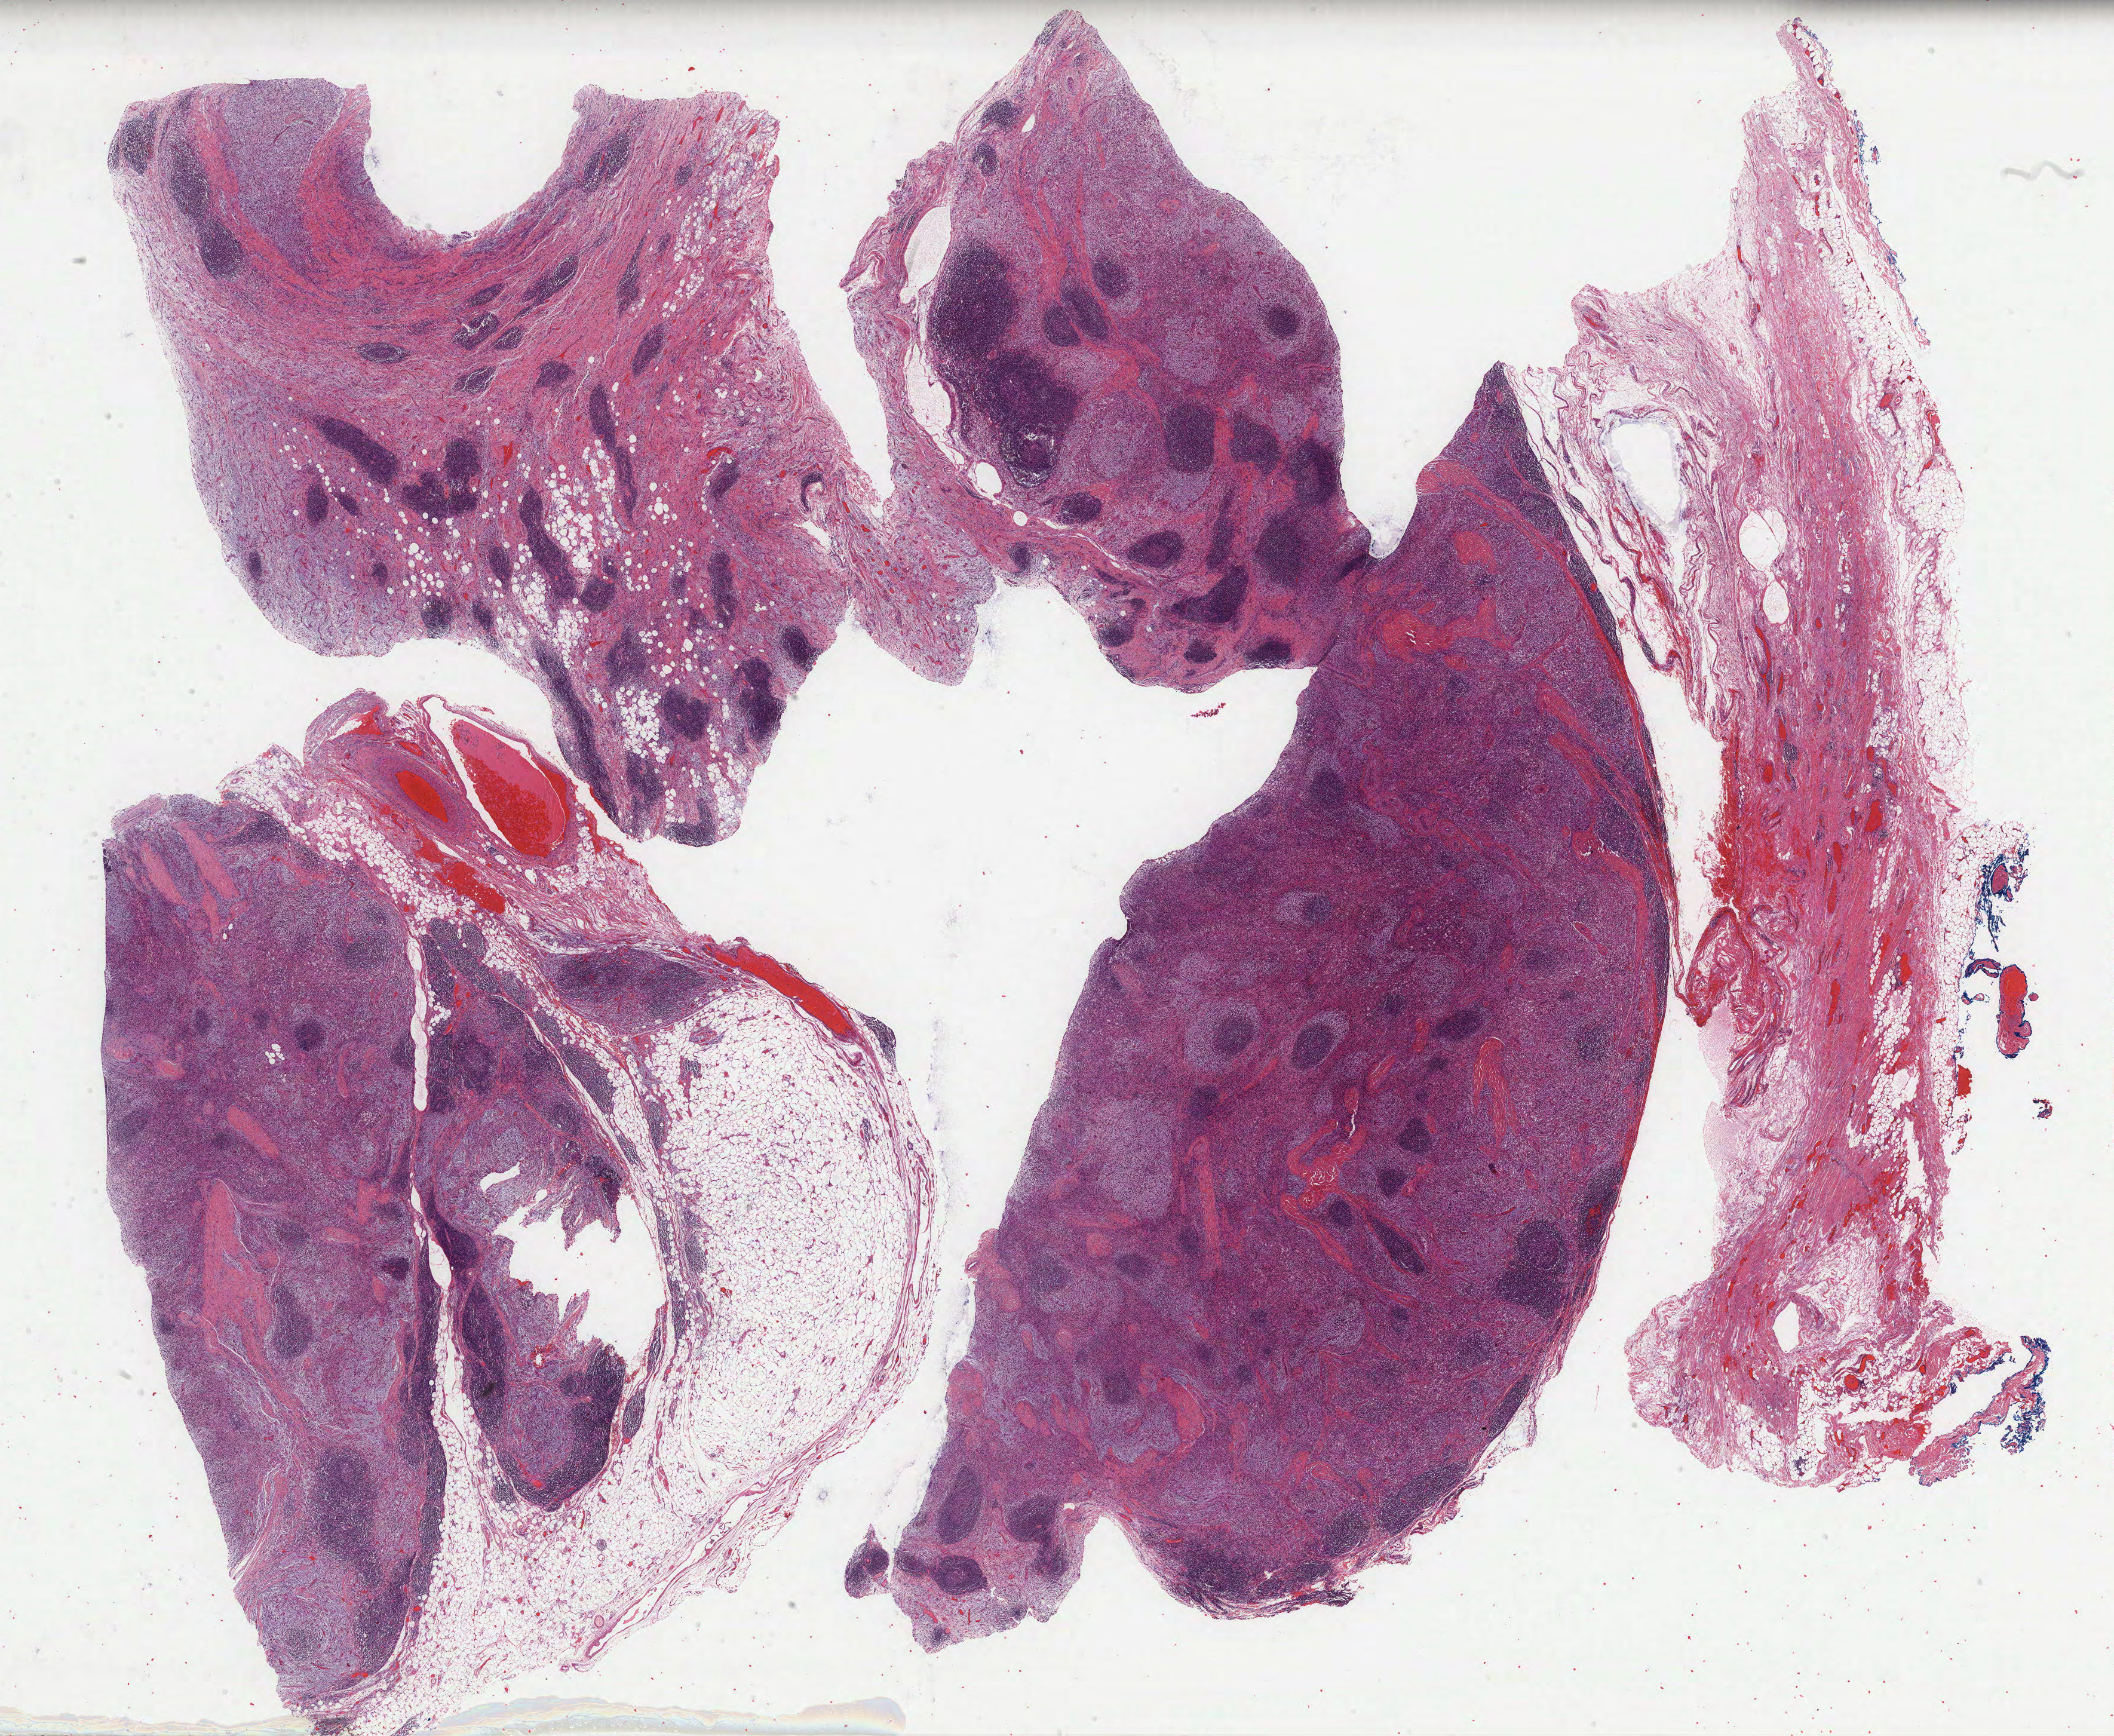
Whole-slide histology image, Hematoxylin and eosin (H&E) stained, low-resolution overview of the scanned area, about 28.6 x 23.5 mm; formalin-fixed paraffin-embedded (FFPE) diagnostic section; primary tumour sample from the connective, subcutaneous and other soft tissues. Male patient; age at initial diagnosis 68 years.
* pathologic diagnosis: Dedifferentiated liposarcoma (connective, subcutaneous and other soft tissues of pelvis)